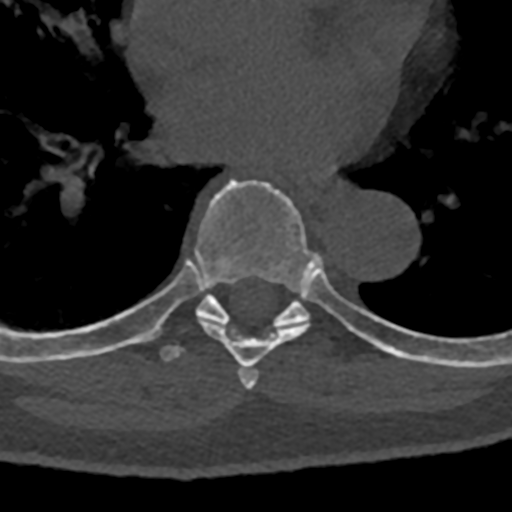
CT including the spine, one axial slice. Position 743 of 797 along the scan axis. Reconstruction kernel Br40s/3. 120 kVp. Bone window (W 1800 / L 400 HU). 0.5 mm slice thickness. 512 × 512 image matrix, field of view 160 × 160 mm. Patient: male, 74 years. From the clinical record (not read from this slice): primary cancer: renal; vertebrae with lytic lesions (as recorded): T10, L1, L2, L3, L4, L5.
Structures marked on this image (semi-automatic segmentation, software-assisted and operator-edited):
- T6 vertebra: bounding box [x1, y1, x2, y2] px = [239, 367, 258, 386]
- T7 vertebra: [108, 179, 394, 389]
- T8 vertebra: [70, 276, 432, 364]